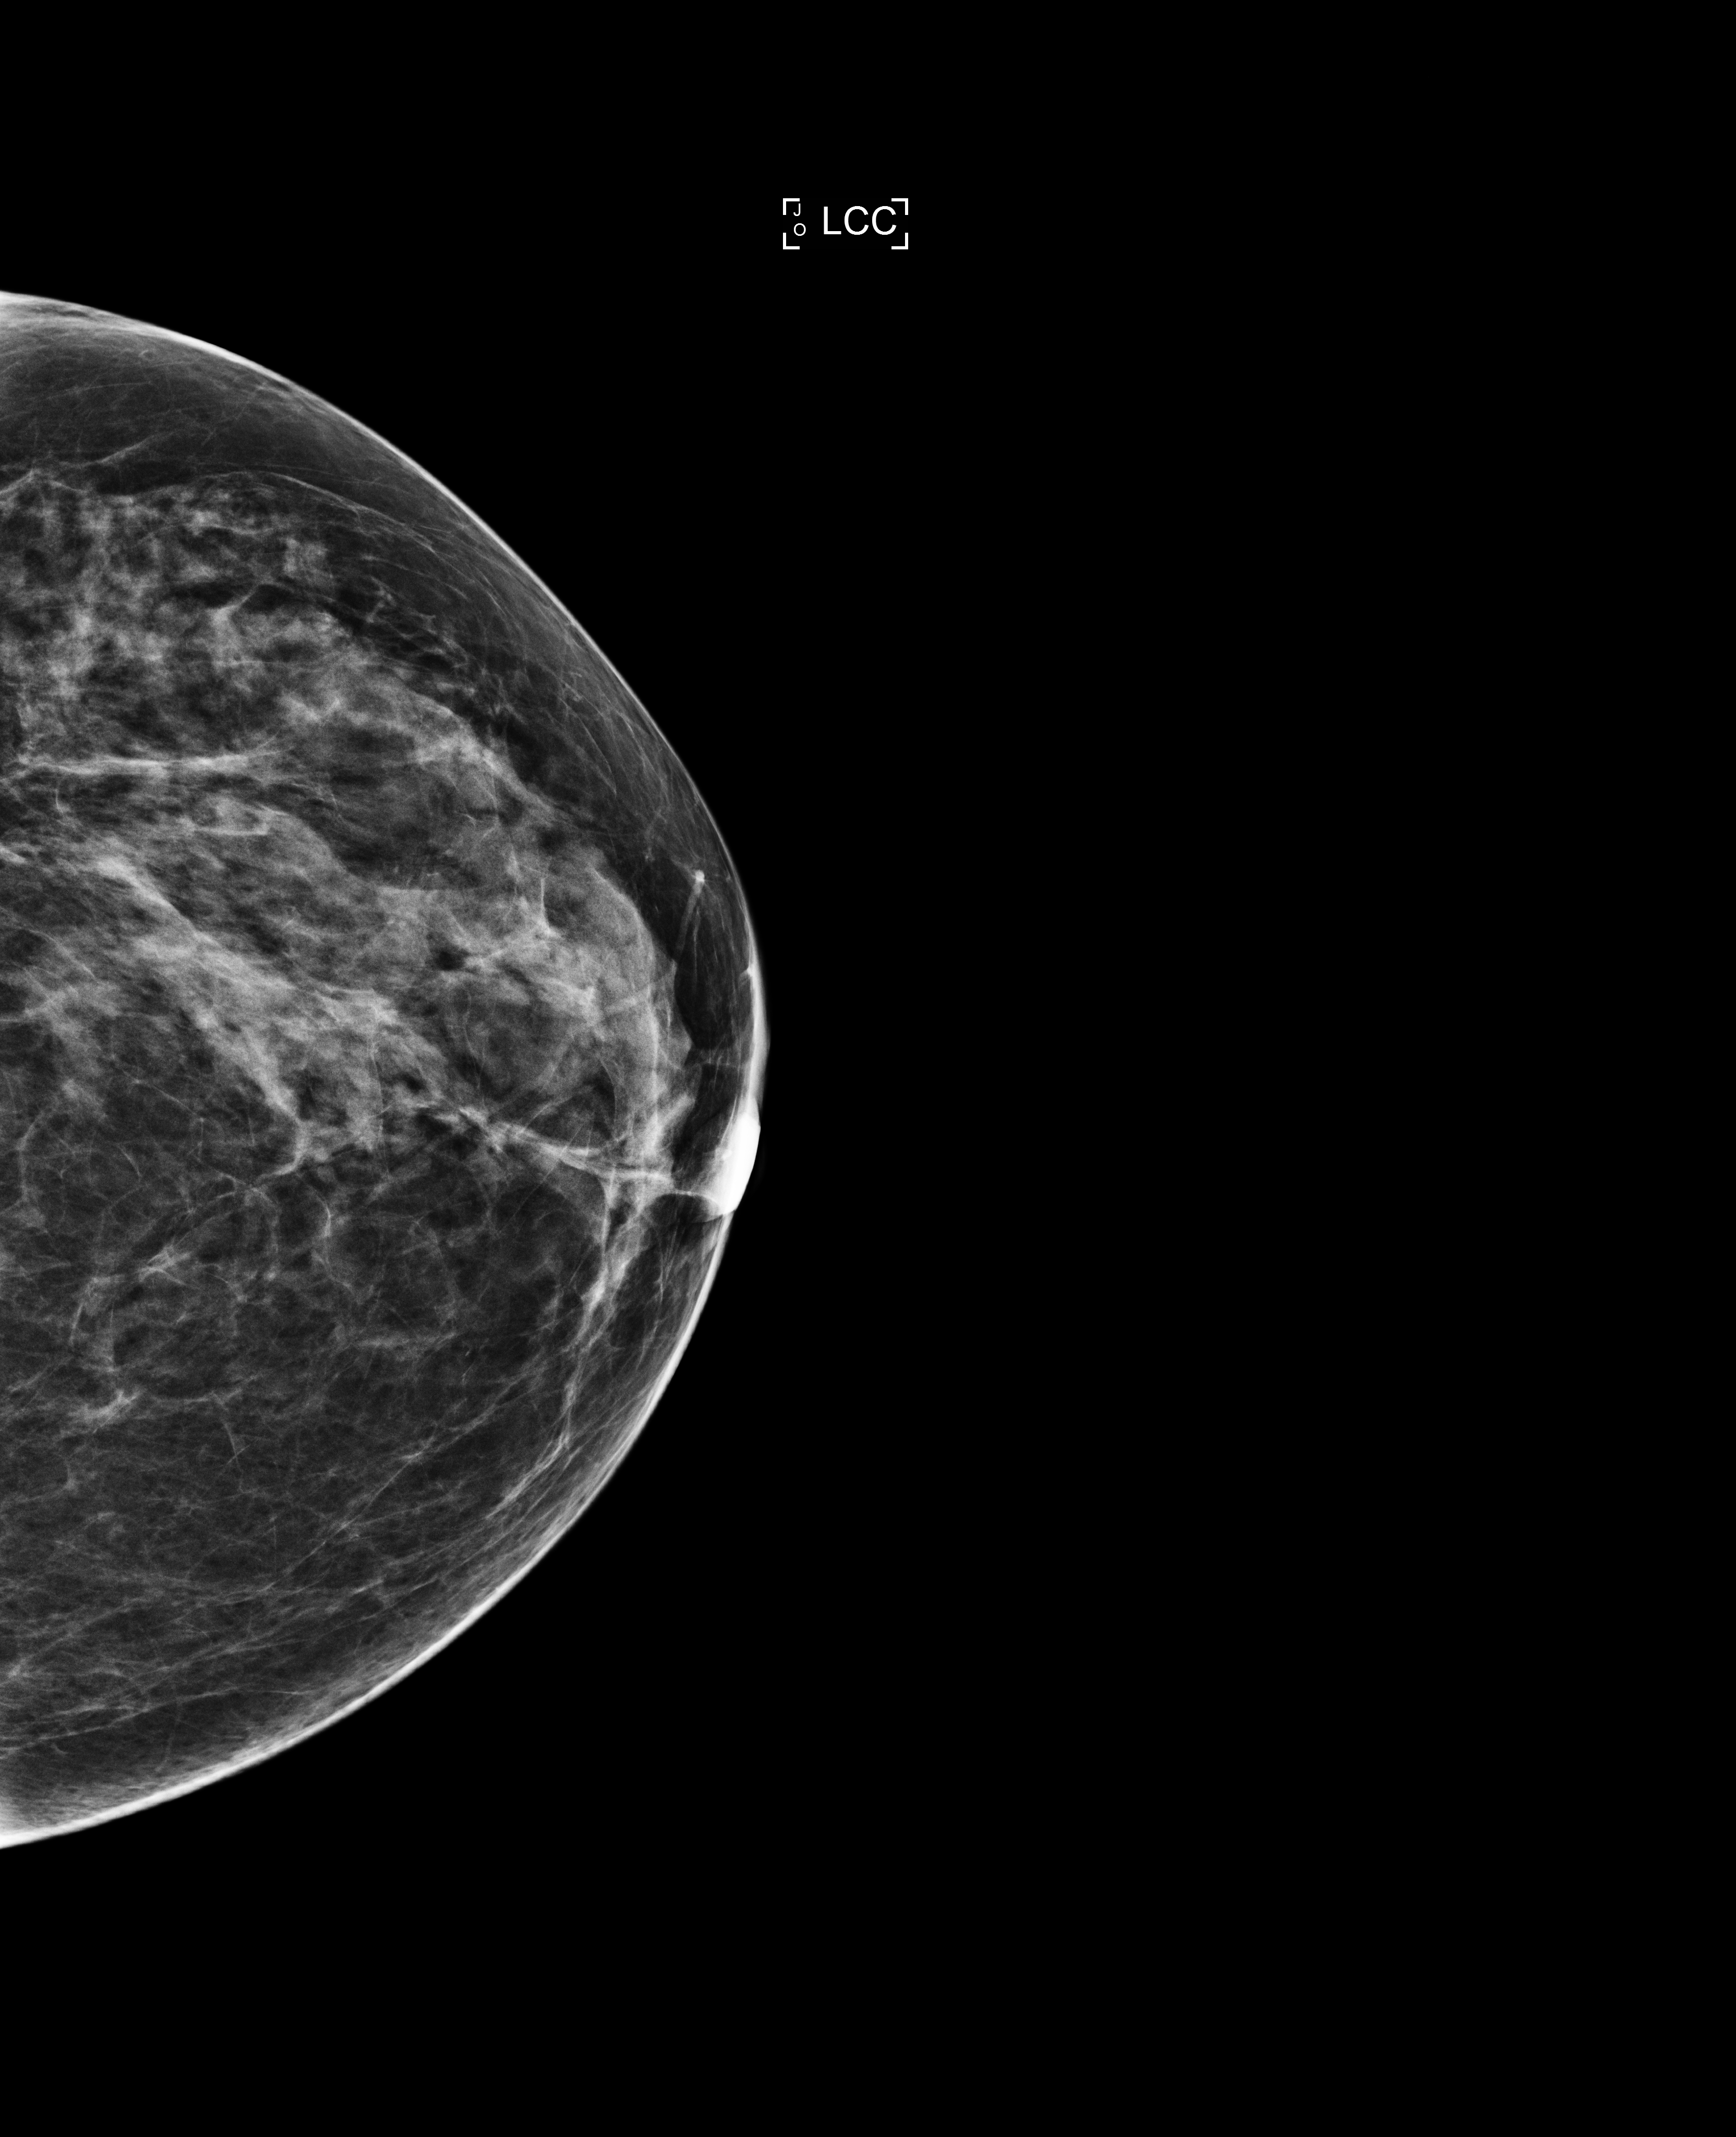
Full-field digital mammogram (FFDM), left breast, cranio-caudal projection, screening examination, system: Selenia Dimensions. Female patient, age 57 years.
BI-RADS breast density category at the screening exam (both breasts, scale 1–4): 3.